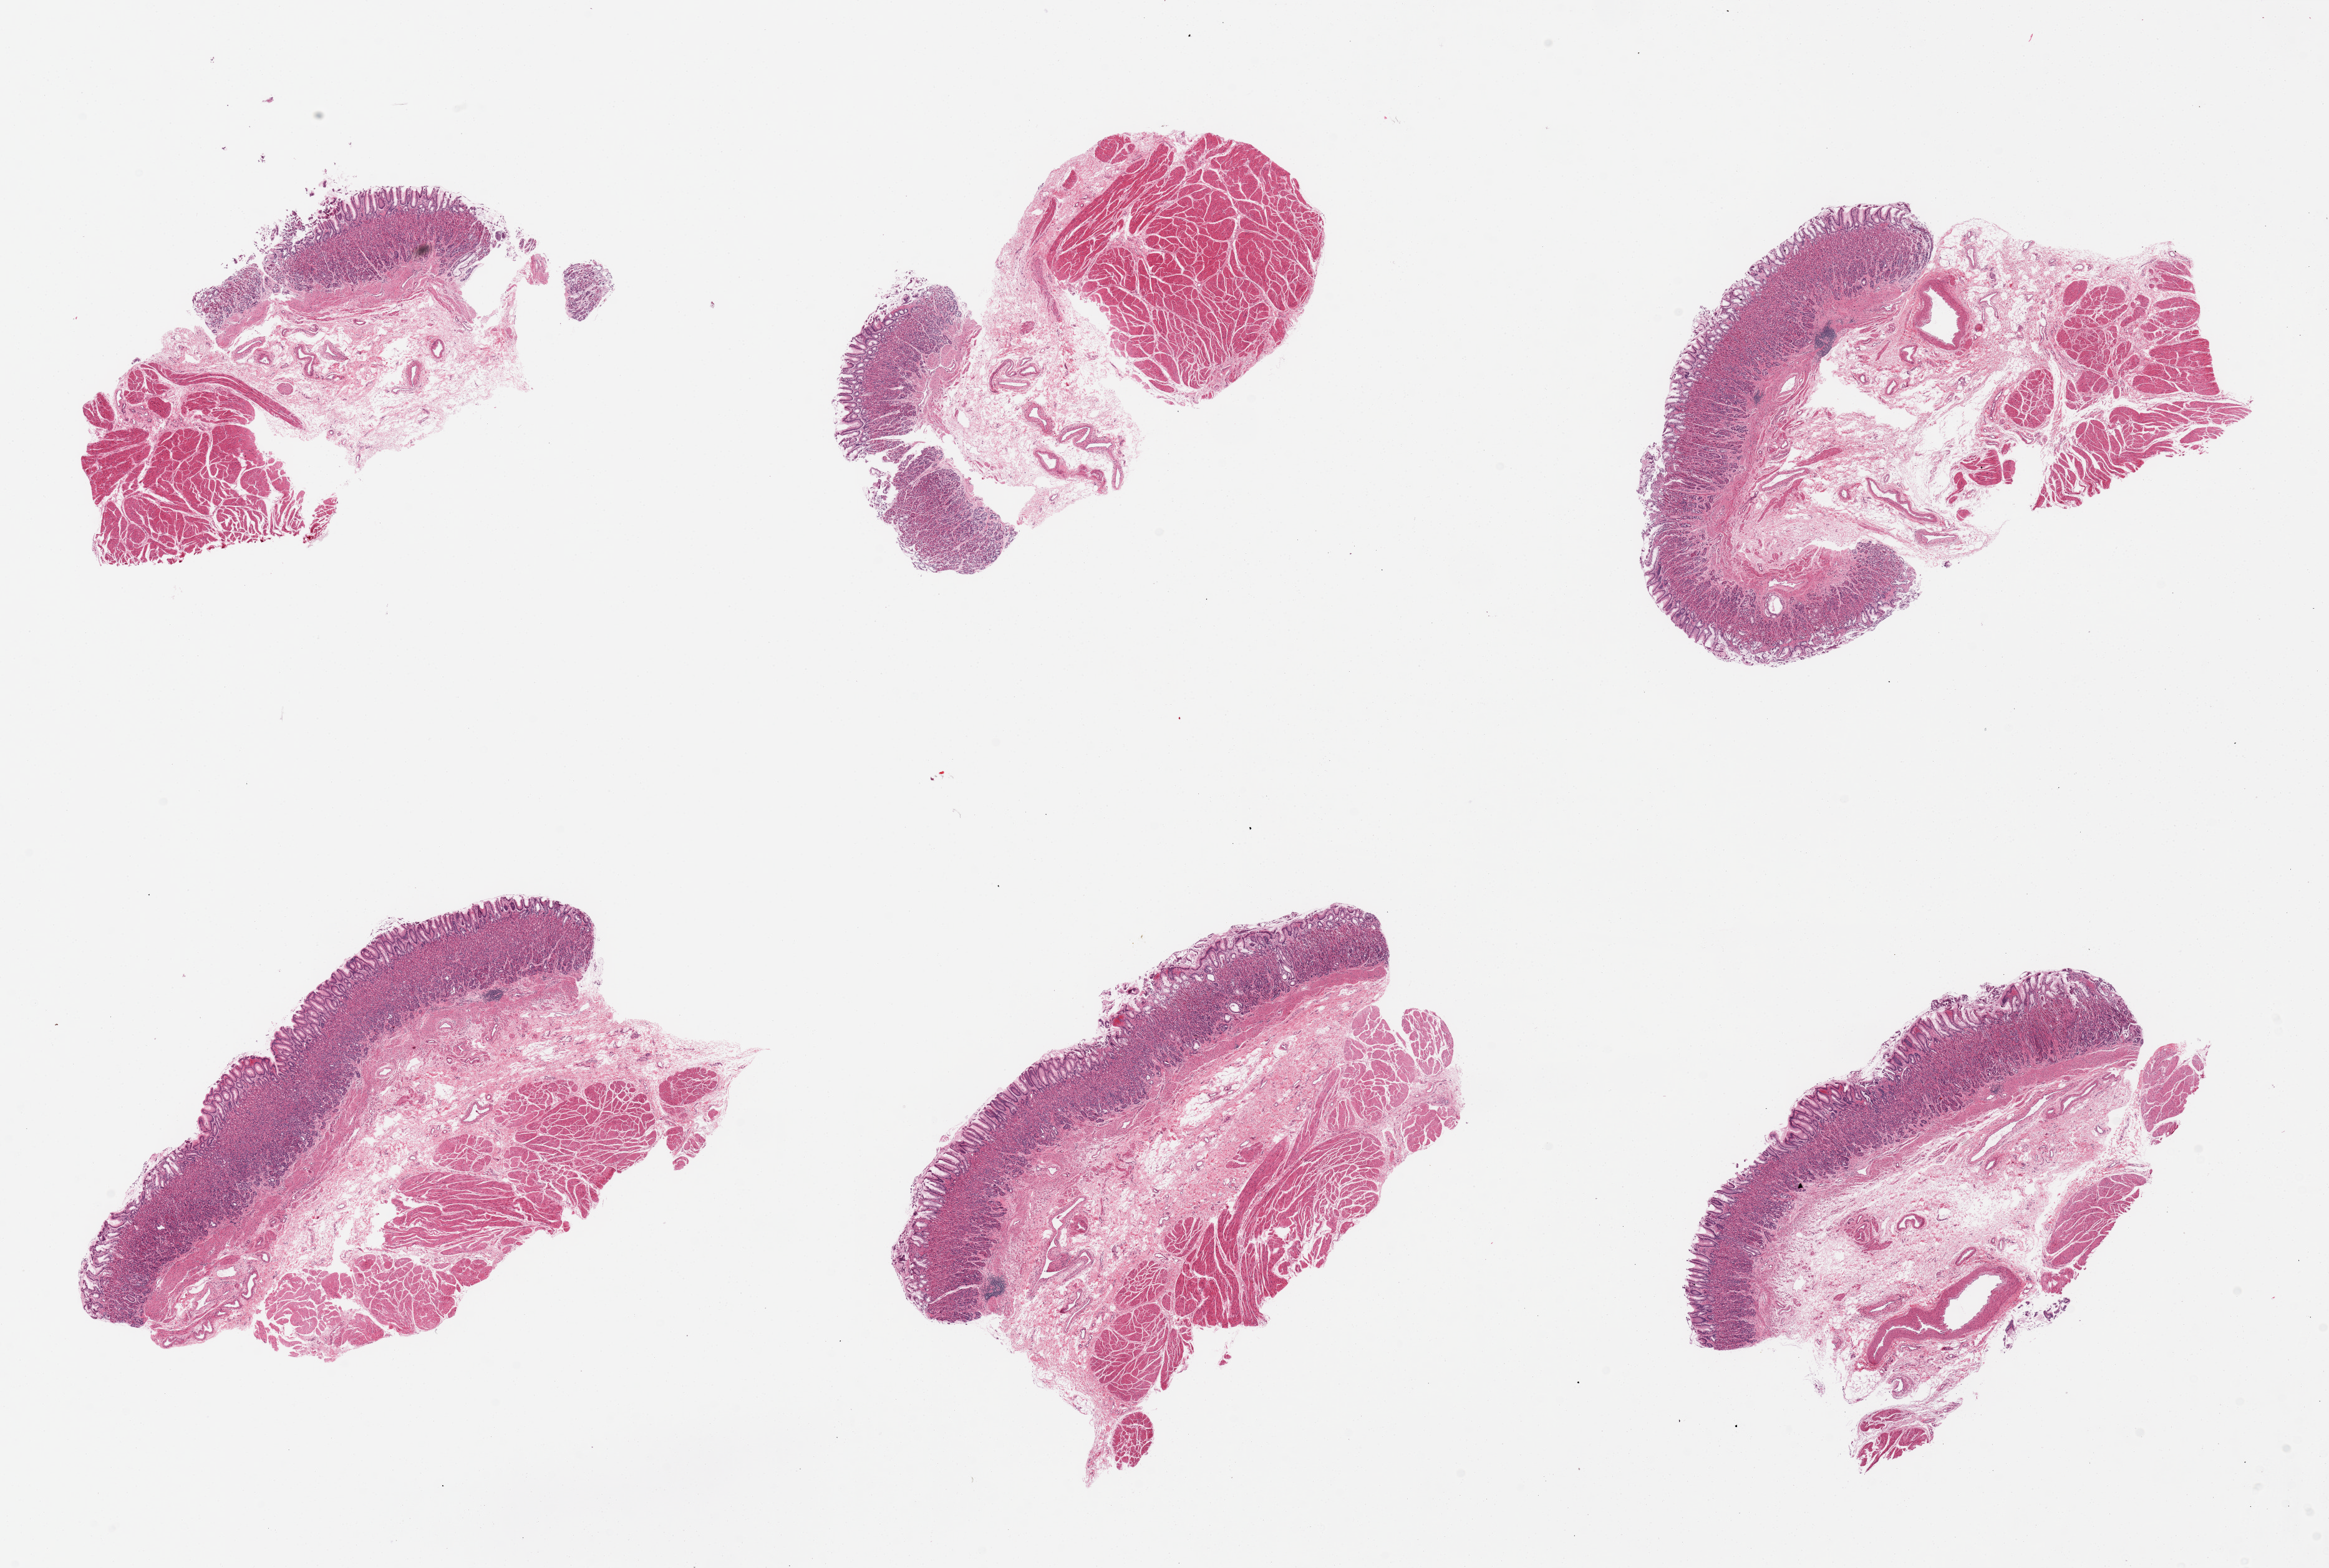
Whole-slide image, hematoxylin and eosin (H&E) stain, whole scanned area (about 29.5 x 19.9 mm, from a 20x scan) shown as a low-resolution overview, PAXgene-fixed paraffin-embedded (PFPE) section, sampled site (target tissue): gastroesophageal junction, donor tissue sample. Donor sex: female.
• pathologist's review note for this sample: 6 pieces, all include gastric mucosa (not target)